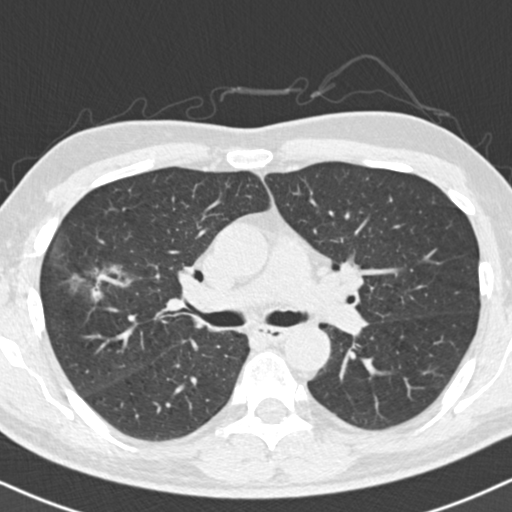
Low-dose screening chest CT, axial slice; baseline annual screen; lung window (W 1500 / L -600 HU); 120 kVp; slice 62 of 154 in the series; 512 × 512 image matrix, field of view 322 × 322 mm. Male participant, aged 56 years at enrolment. Former smoker at enrolment.
• Expert-annotated lung lesion, bounding box (x1, y1, x2, y2) in pixels: (54, 253, 144, 318).
• No non-calcified nodule or mass ≥4 mm was recorded by the screening reader at this exam.
• Participant outcome: lung cancer diagnosed 392 days after this screen — bronchiolo-alveolar adenocarcinoma, NOS, right upper lobe, well differentiated (G1), stage IIB (AJCC 6th edition), 30 mm at pathology.